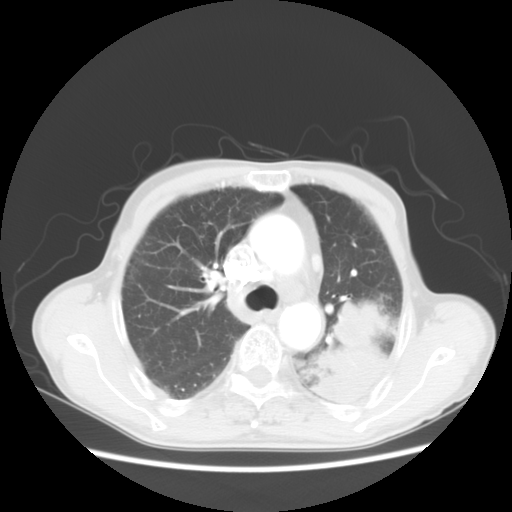
Chest CT, one axial slice; position 36 of 51 along the scan axis; lung window (W 1500 / L -600 HU); 512 × 512 image matrix, field of view 360 × 360 mm. Male patient, age 64 years. From the clinical record (not read from this slice): clinical TNM (as recorded): T4 N0 M0; histopathological grade: G2-3.
Structures marked on this image (rectangle marked by the reading radiologist):
- lung tumour (recorded histology: squamous cell carcinoma): bounding box <327,286,383,395> (left, top, right, bottom; pixels)